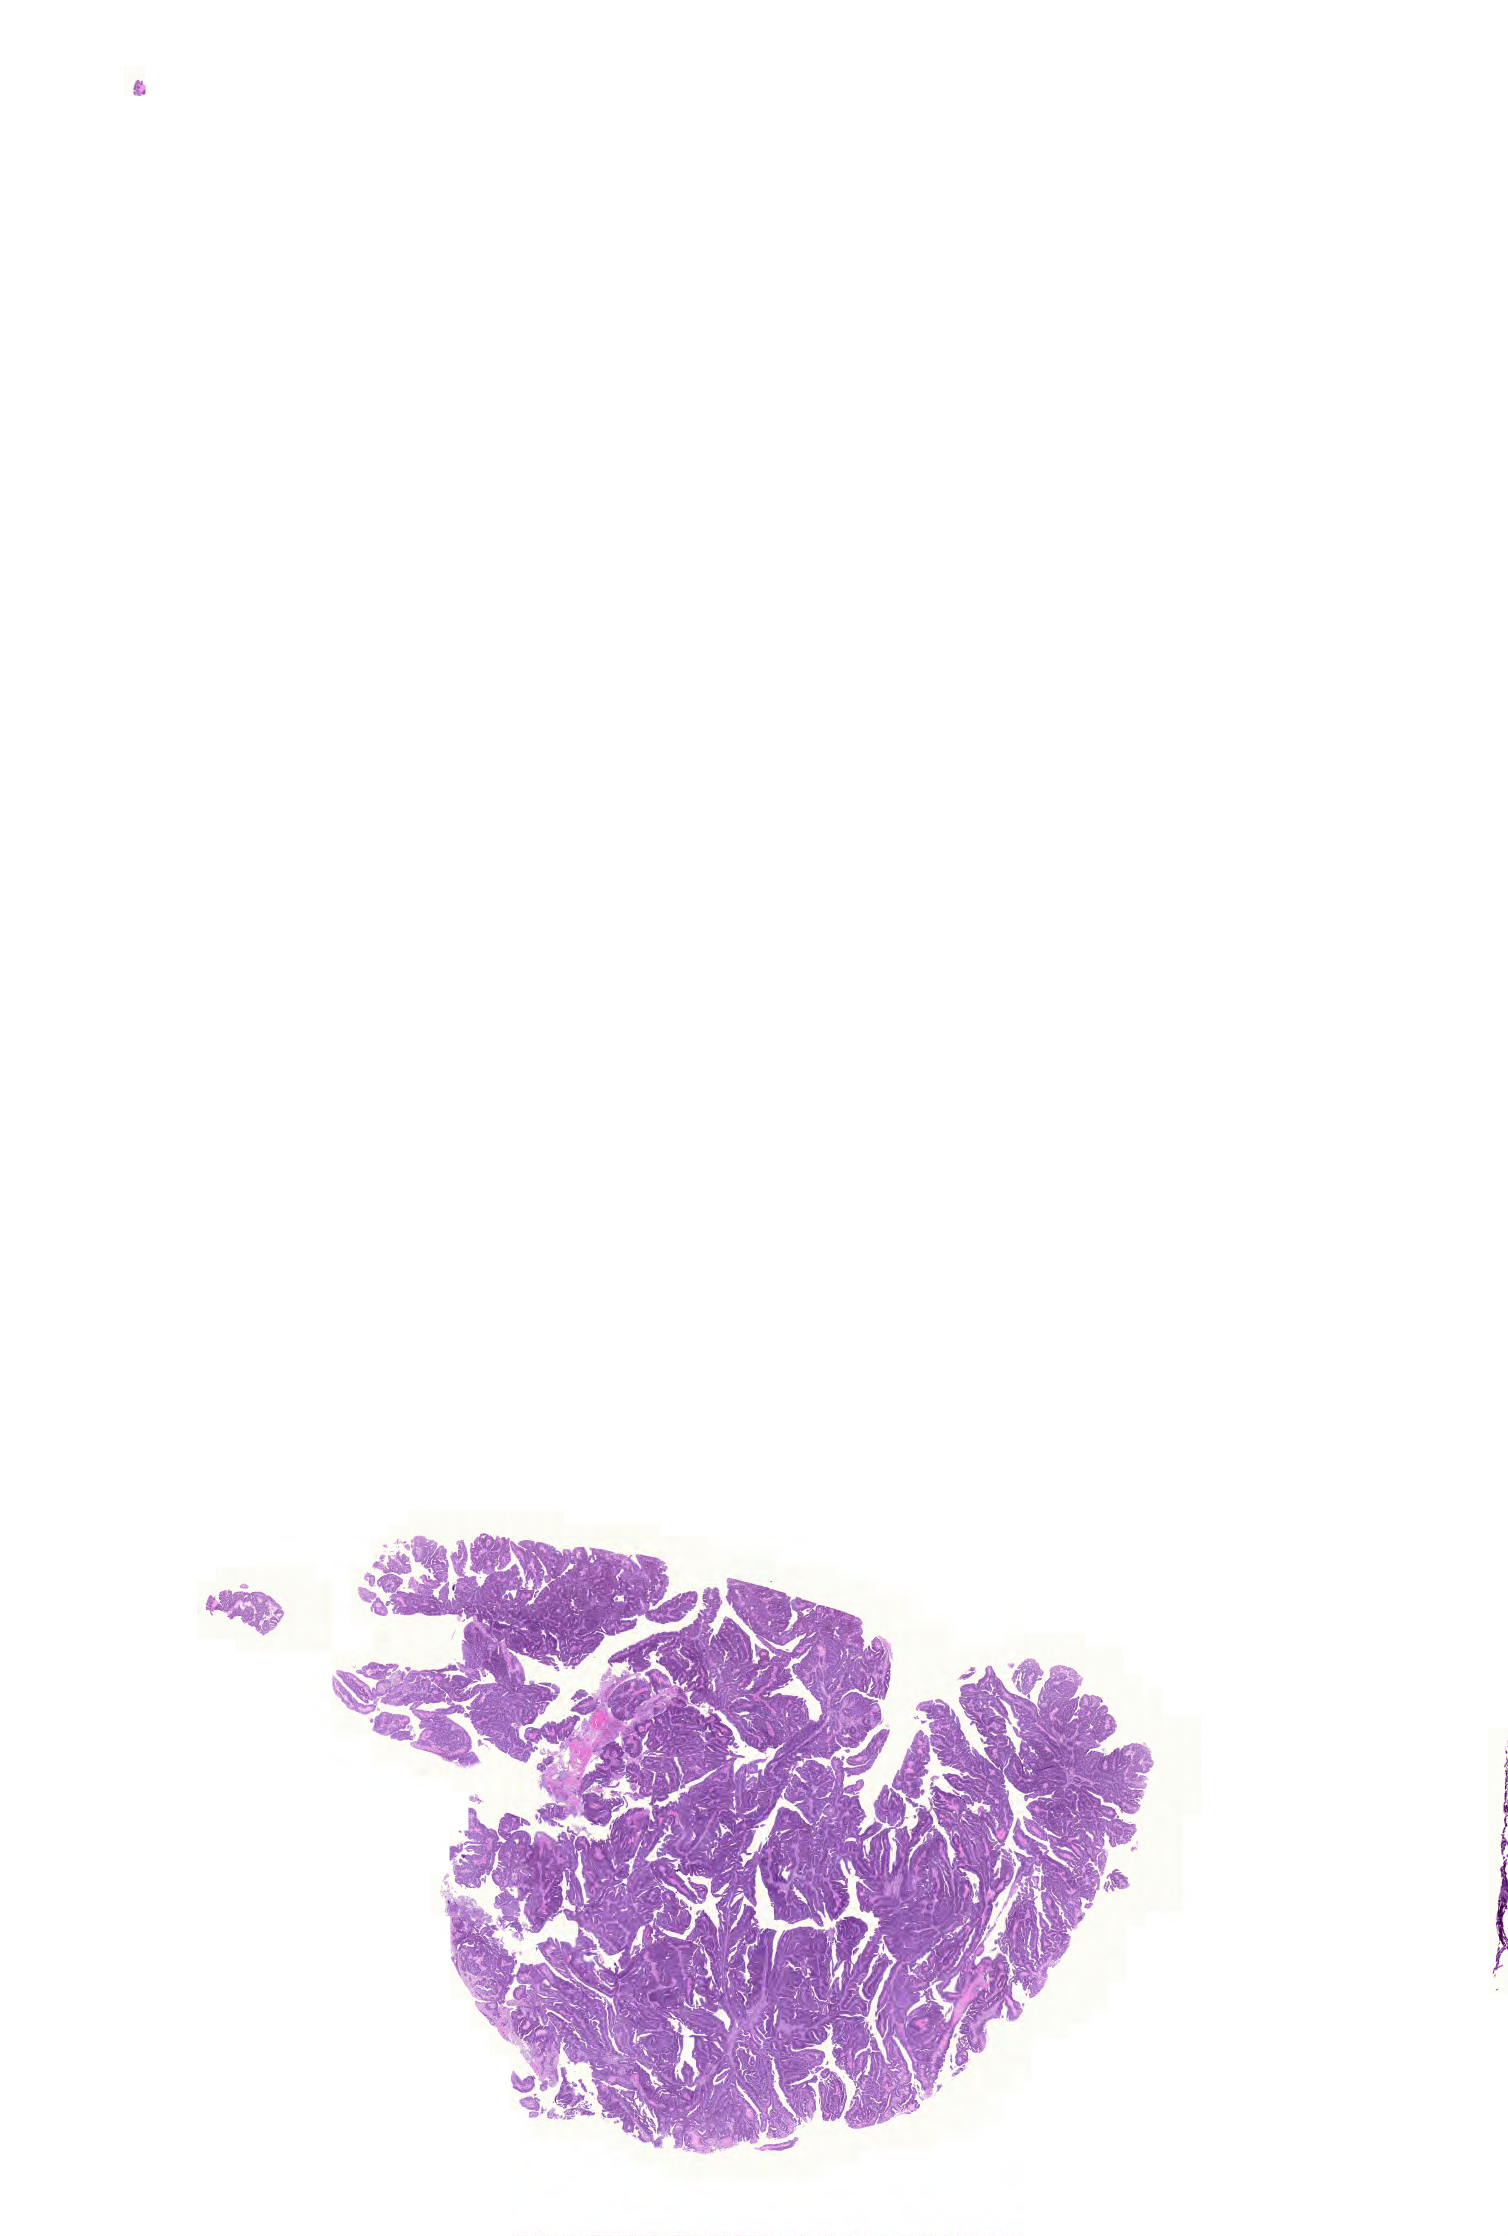
Whole-slide histology image, H&E, whole scanned area (about 22.4 x 33.3 mm, acquisition: 20x scan) shown as a low-resolution overview; formalin-fixed paraffin-embedded (FFPE) diagnostic section; sample: primary tumour, colon. Female patient; age at initial diagnosis 74 years.
Histologic diagnosis: Adenocarcinoma, NOS (ascending colon).